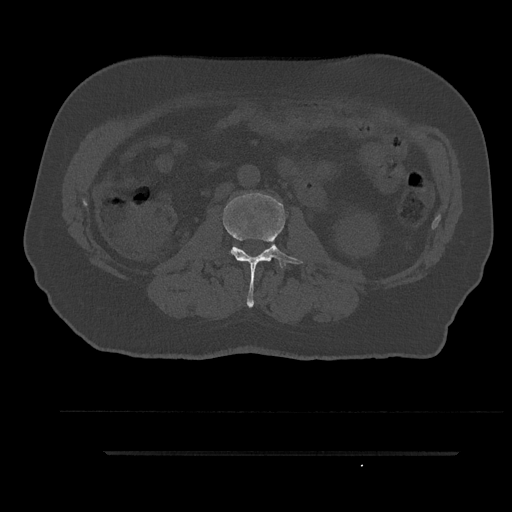
CT including the spine, one axial slice; position 101 of 797 along the scan axis; bone window (W 1800 / L 400 HU); 0.5 mm slice thickness; 512 × 512 image matrix, field of view 432 × 432 mm. Patient: male, 63 years. From the clinical record (not read from this slice): primary cancer: renal.
Annotated regions visible in this slice (semi-automatic segmentation, software-assisted and operator-edited):
- L2 vertebra: bounding box [x1, y1, x2, y2] px = [223, 193, 304, 307]